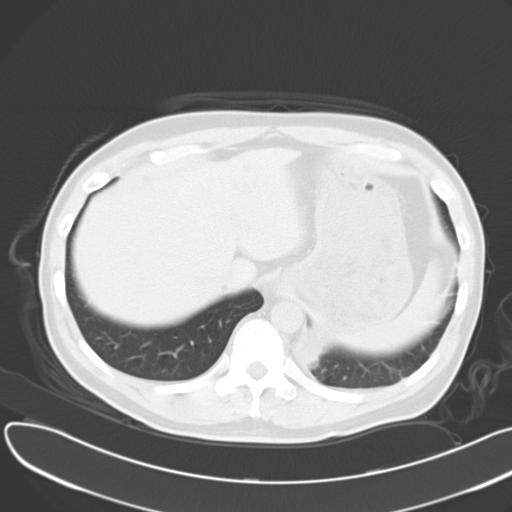
Chest CT, one axial slice; slice 6 of 30 in the series (ordered by position); reconstruction kernel B40f; lung window (W 1500 / L -600 HU); 10 mm slice thickness; 512 × 512 image matrix, field of view 376 × 376 mm. Patient: male, 55 years. From the clinical record (not read from this slice): clinical TNM (as recorded): T2 N3 M0; histopathological grade: G3.
Structures marked on this image (rectangle marked by the reading radiologist):
- lung tumour (recorded histology: small cell carcinoma): bounding box (x1, y1, x2, y2) in pixels: (297, 324, 329, 367)